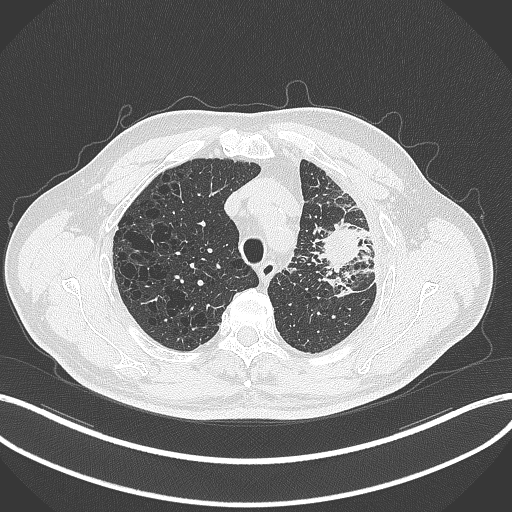
Chest CT, one axial slice; slice 253 of 297 in the series (ordered by position); reconstruction kernel B70f; lung window (W 1500 / L -600 HU); 512 × 512 image matrix. Patient: male, 68 years. Case-level facts recorded for this patient, not image findings: clinical TNM (as recorded): T3 N3 M1.
Outlined on this slice (rectangle marked by the reading radiologist):
- lung tumour (recorded histology: adenocarcinoma): box from (x=312, y=215) to (x=364, y=281) px